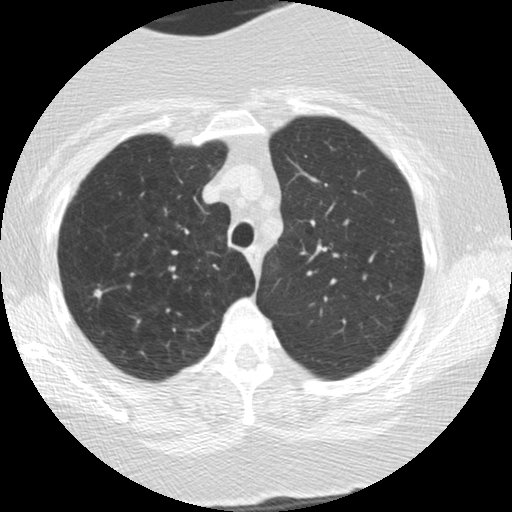
Low-dose screening chest CT, one axial slice; position 135 of 166 along the scan axis; lung window (W 1500 / L -600 HU); 512 × 512 image matrix.
Annotated regions visible in this slice (manually delineated by an expert):
- lesion 2 (tumor, upper lobe of right lung): box from (x=94, y=289) to (x=103, y=298) px